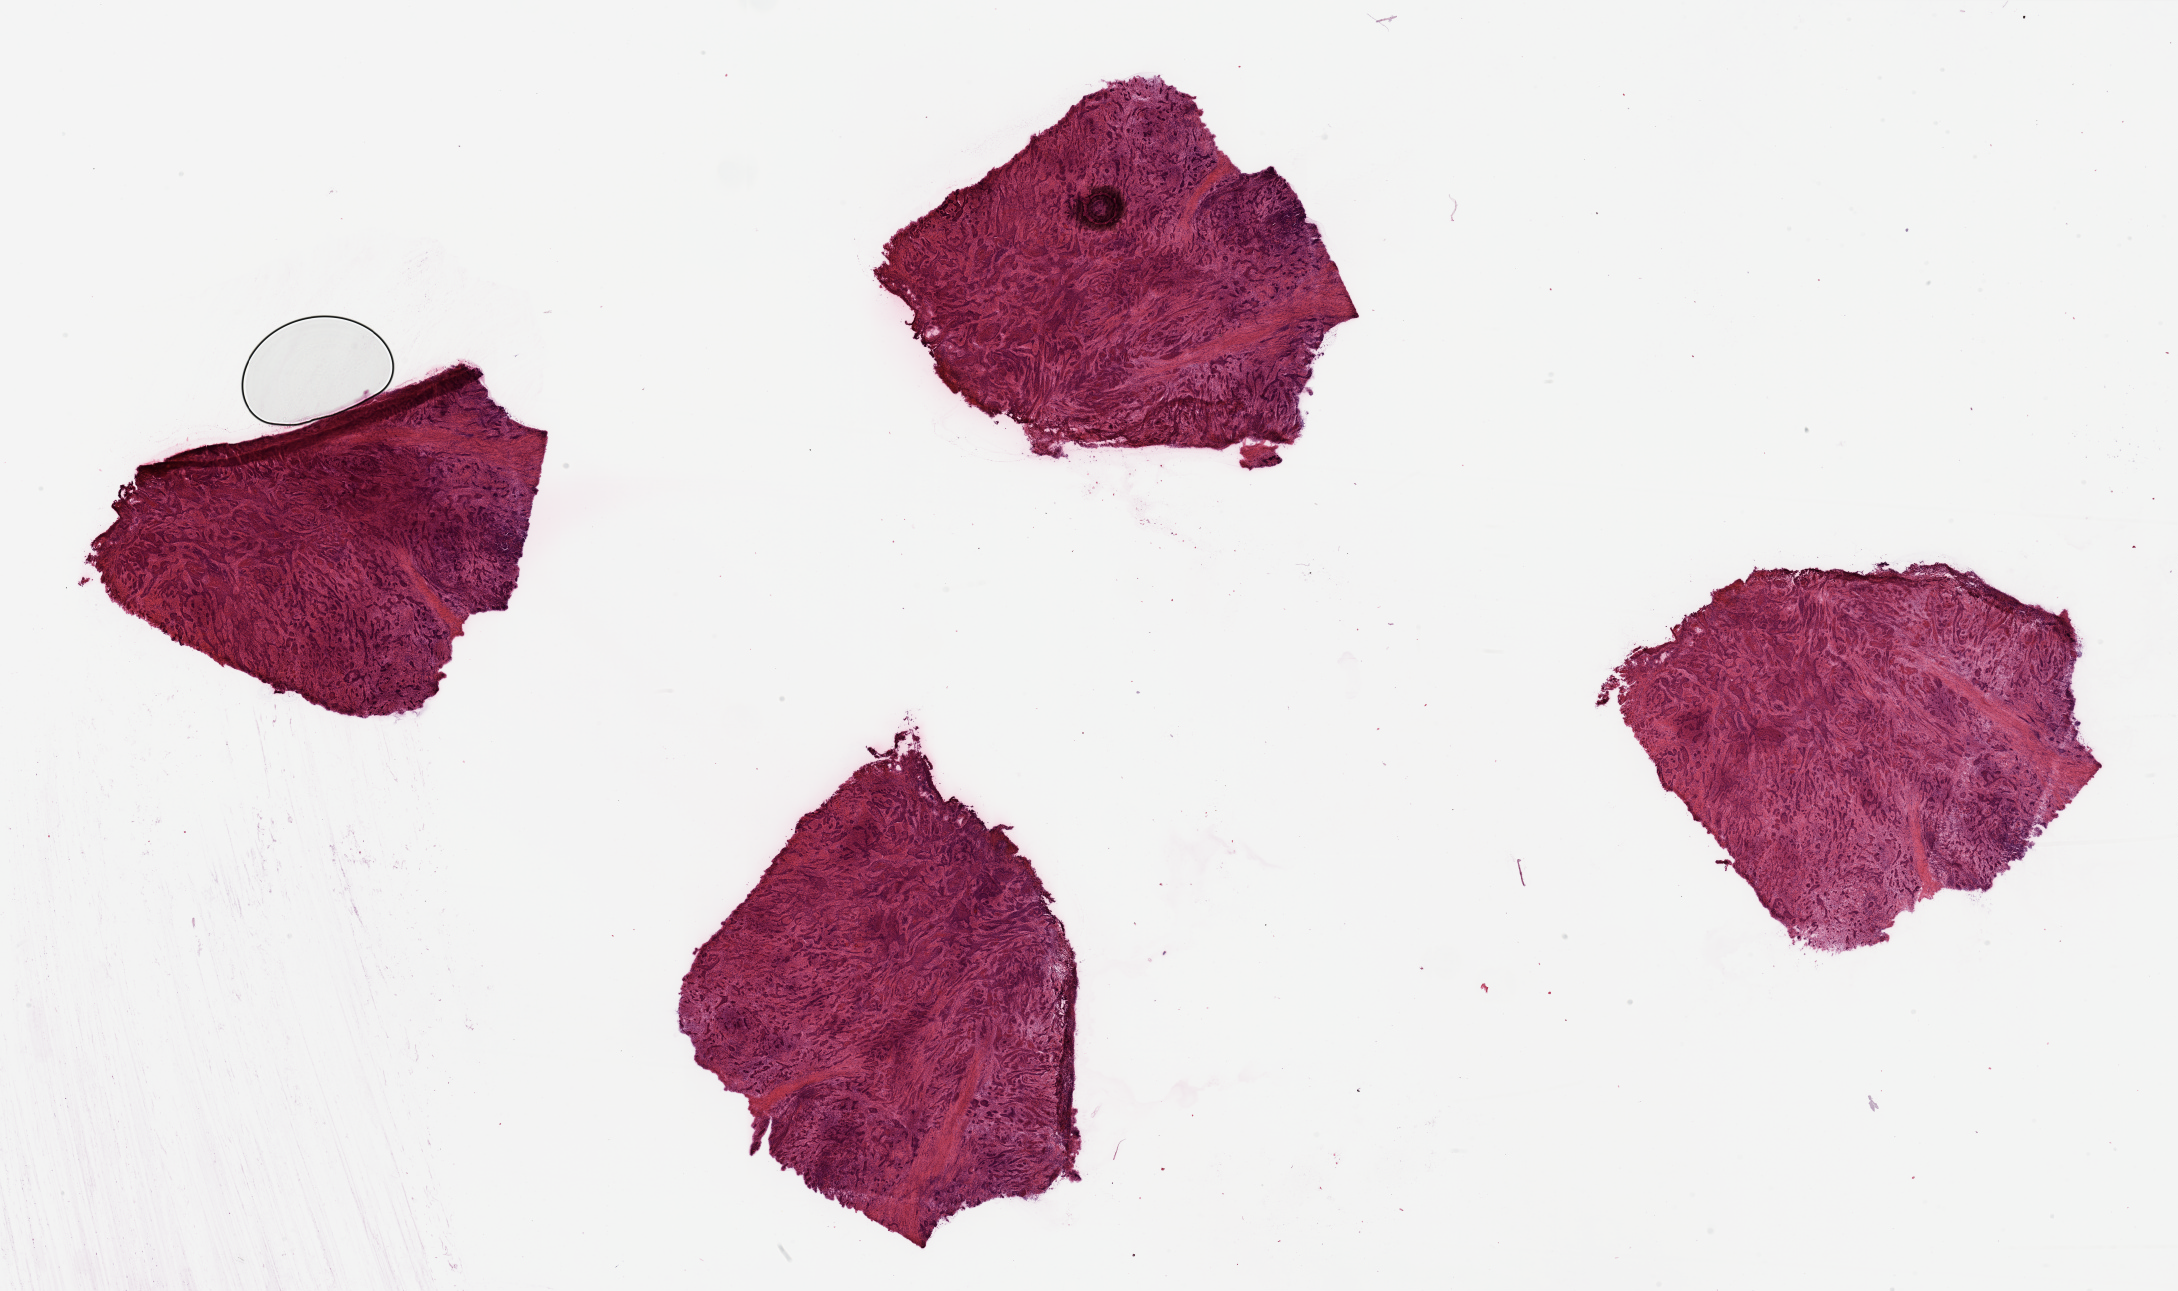
Digitized H&E-stained tissue section (whole slide), whole scanned area (about 34.5 x 20.4 mm) shown as a low-resolution overview; head and neck, tissue type not recorded. Male, 70 y/o.
• patient diagnosis: Squamous cell carcinoma, NOS (larynx, NOS)